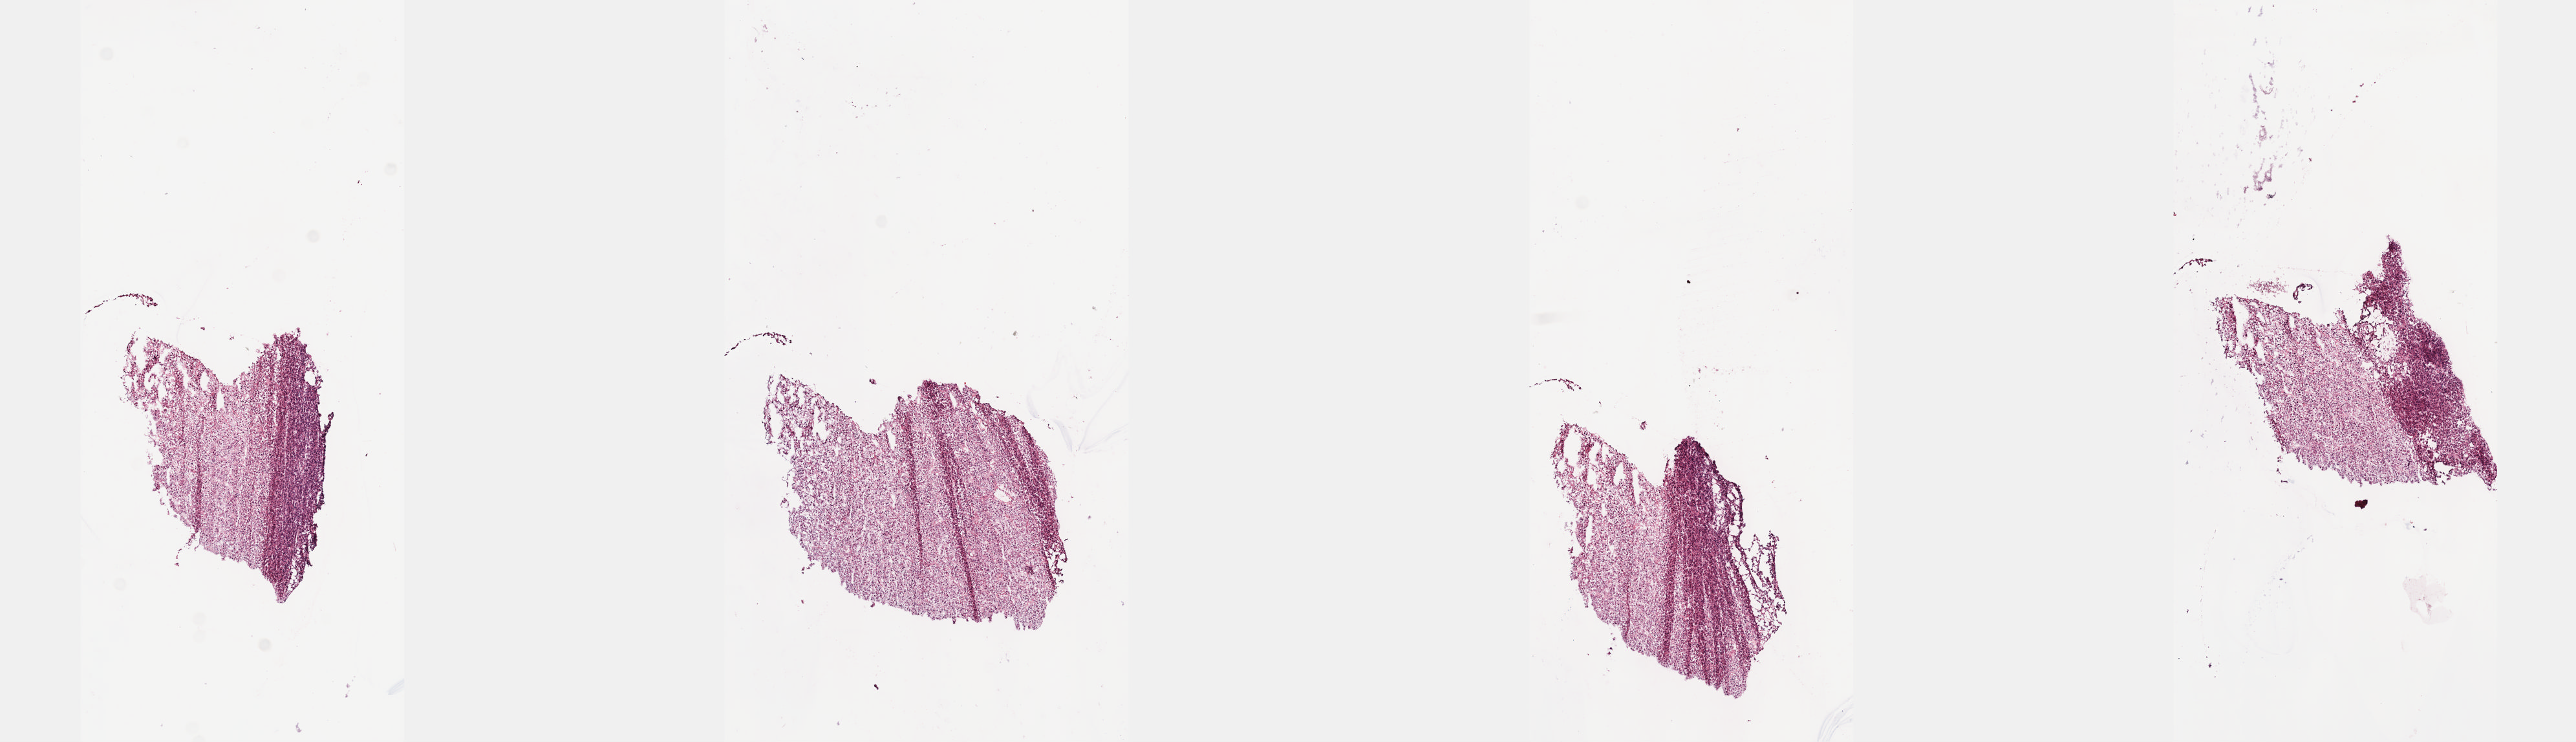
Digitized Hematoxylin and eosin (H&E) stained tissue section (whole slide), low-resolution overview of the scanned area, about 16.1 x 4.6 mm (acquisition: 40x scan), frozen section from the top of the tissue portion, primary tumour sample from the adrenal gland. Male patient; age at initial diagnosis 64 years. Composition of this section per pathologist review: tumour cells 100%, tumour nuclei 80%, normal cells 0%, stromal cells 0%, necrosis 0%. Inflammatory infiltration, as recorded: lymphocyte infiltration 1%, monocyte infiltration 0%, neutrophil infiltration 0%.
• histologic diagnosis: Pheochromocytoma, NOS
• laterality: right